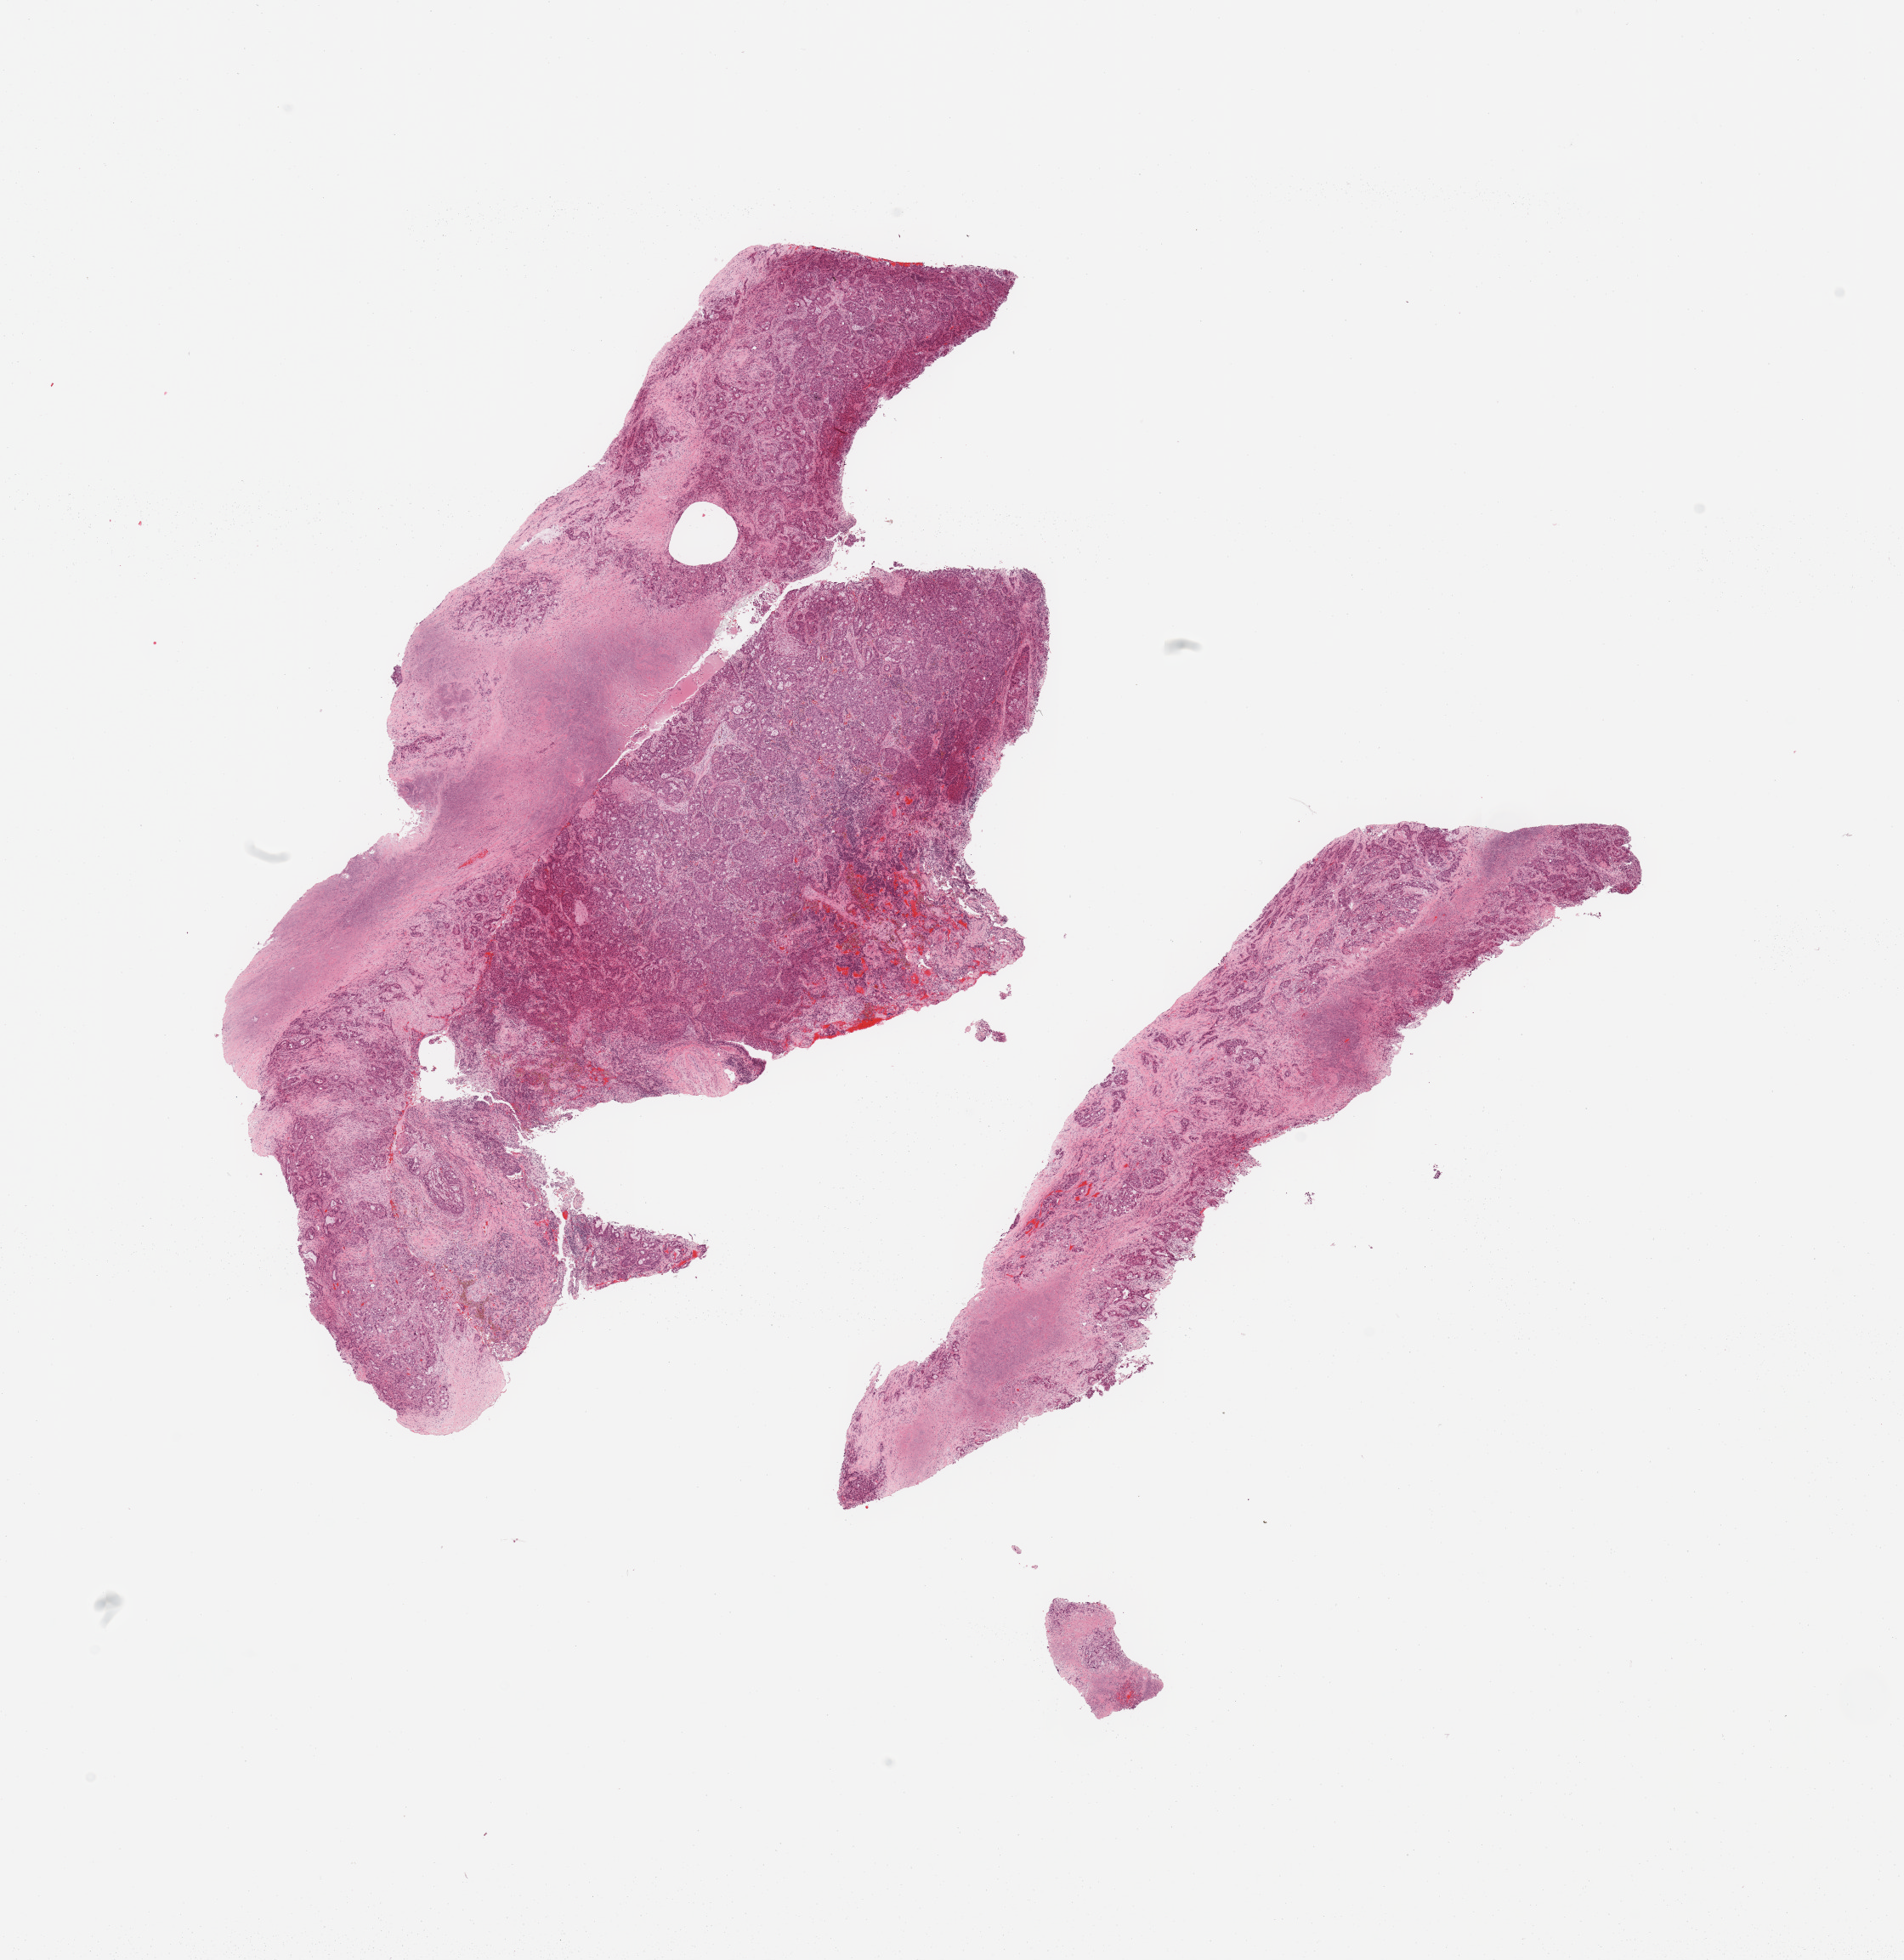
Digitized Hematoxylin and eosin (H&E) stained tissue section (whole slide) — shown as a low-resolution overview of the whole scanned area (about 17.7 x 18.2 mm, acquisition: 20x scan). Lung, tumour tissue. Male, 66 y/o. Histologic grade: G2 (moderately differentiated).
* histologic diagnosis: Adenocarcinoma, NOS
* AJCC pathologic stage: IIIA